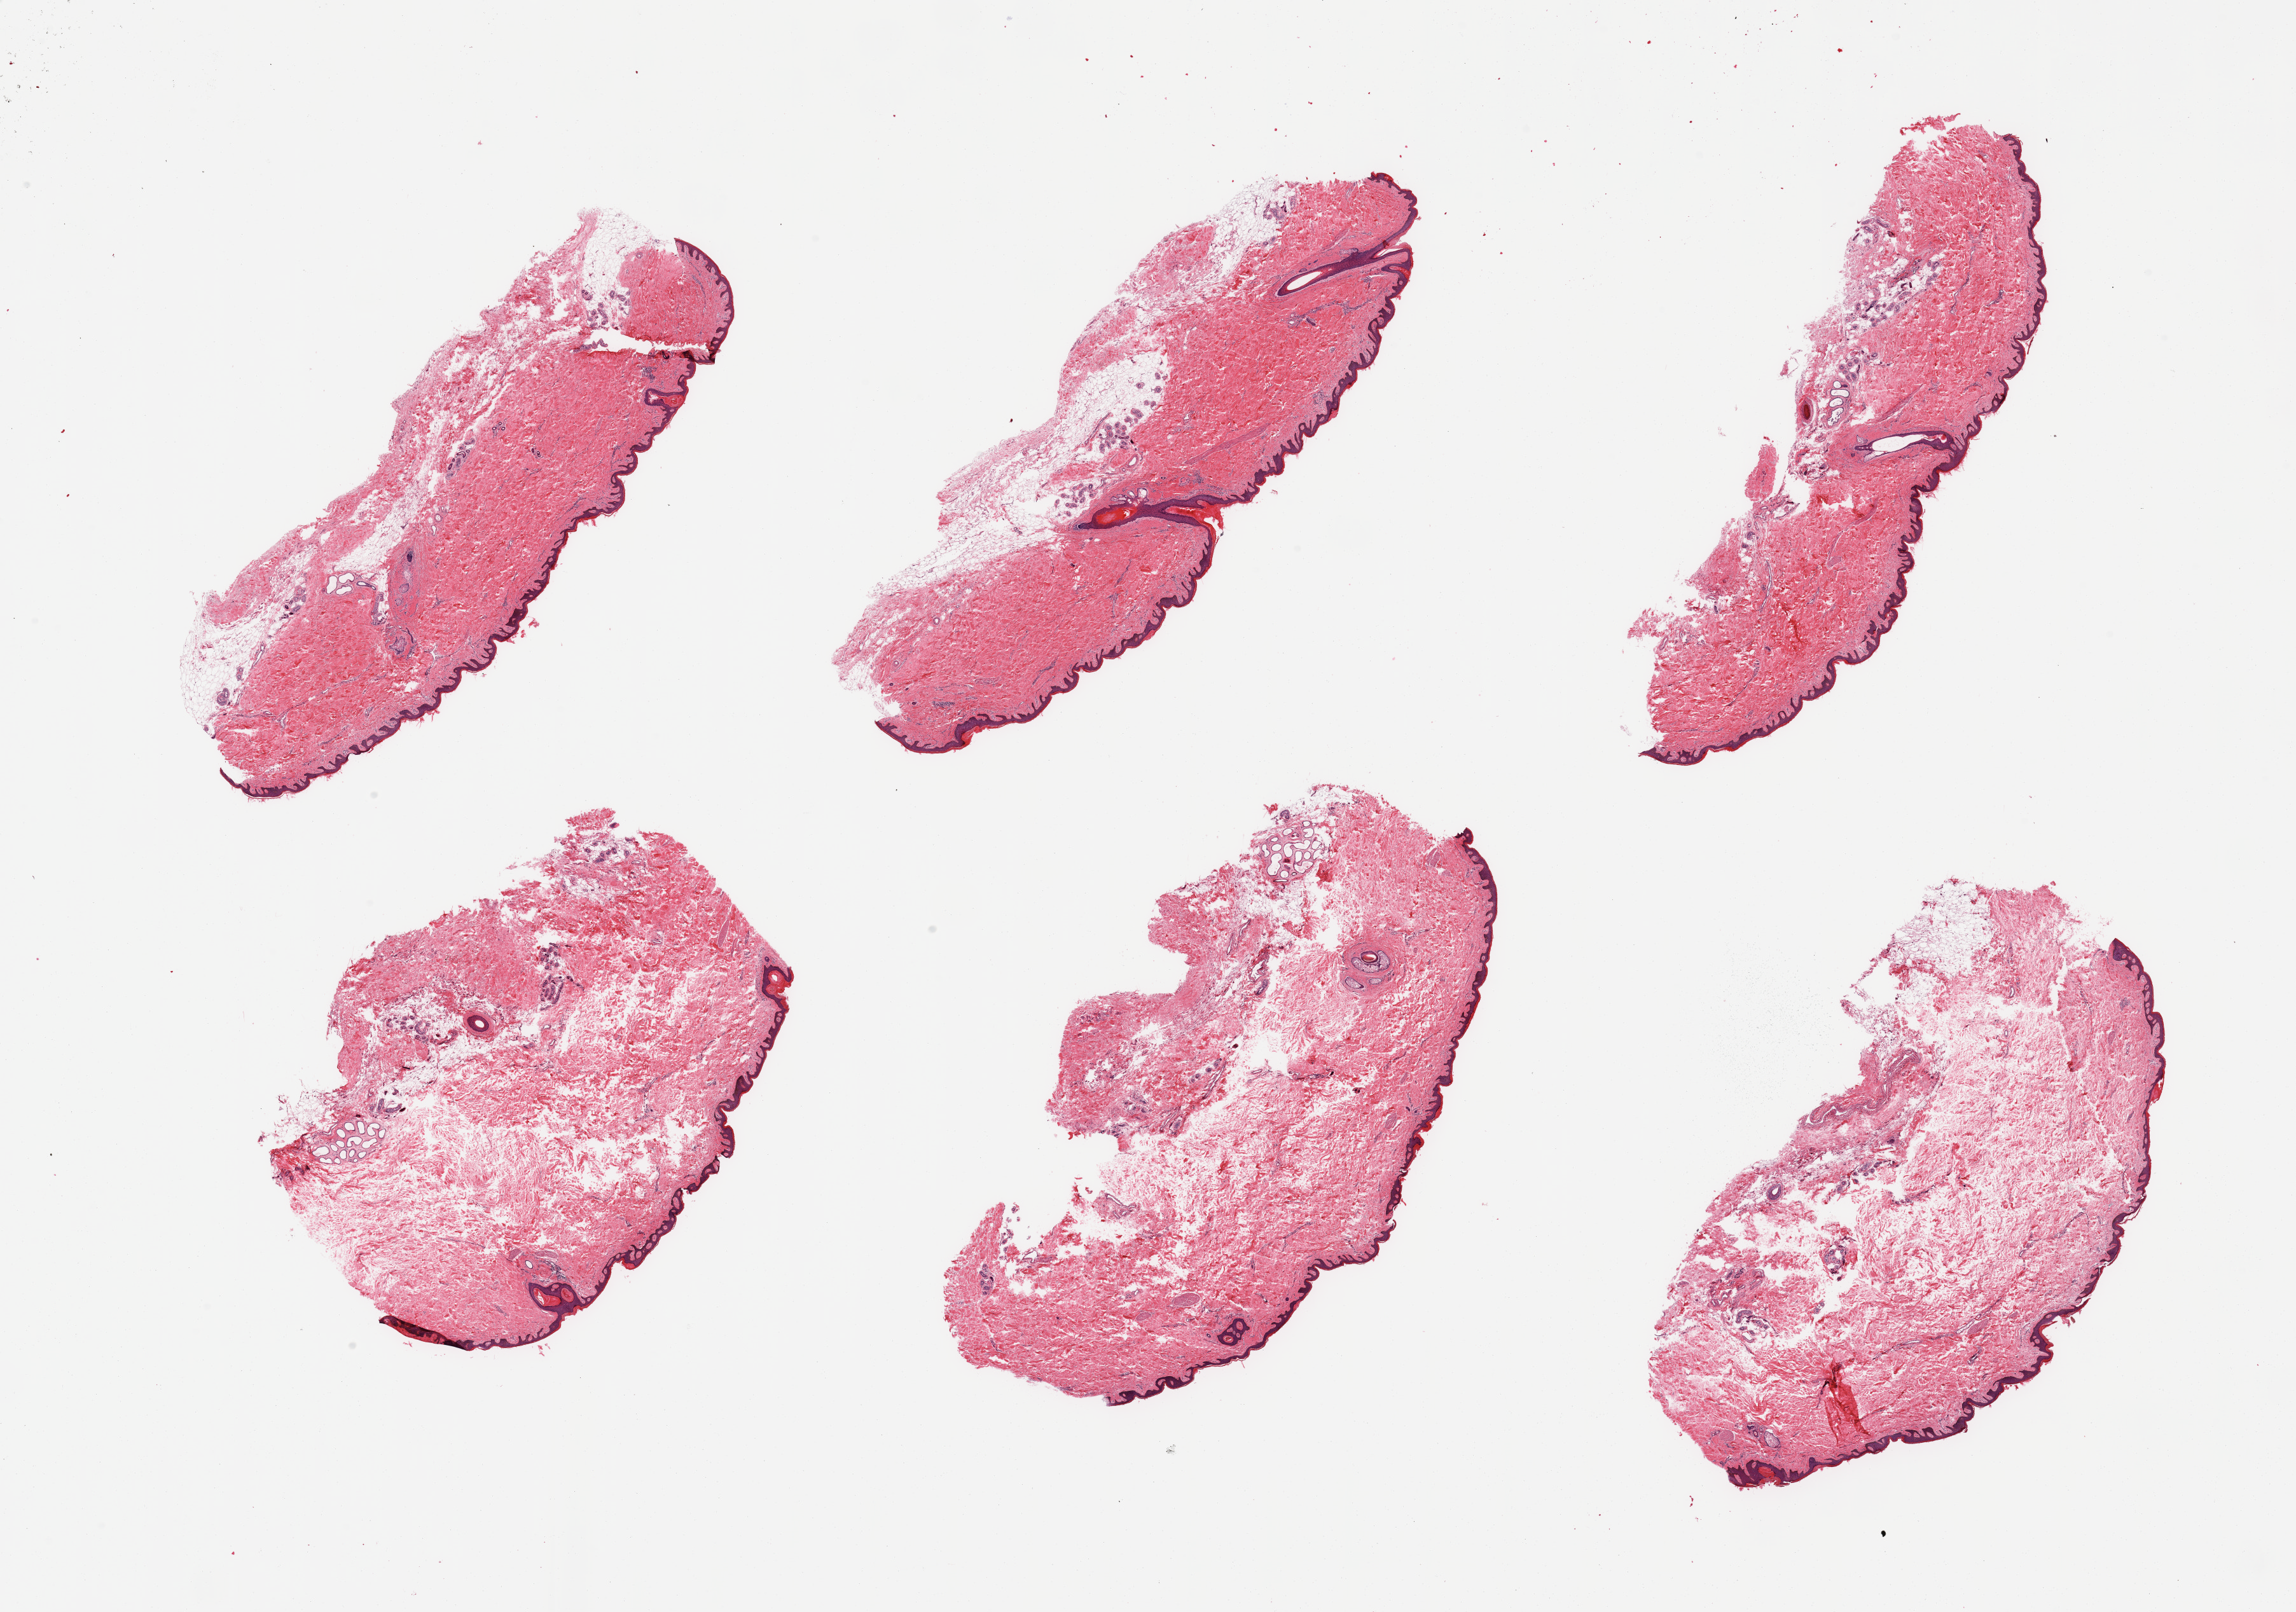
Whole-slide image, hematoxylin and eosin (H&E) stain — a low-resolution overview of the entire scanned area, about 28.5 x 20.0 mm (slide scanned at 20x), PAXgene-fixed paraffin-embedded (PFPE) section, section of skin of suprapubic region (target tissue), tissue donor sample. Donor sex: female.
Reviewer comment on this tissue sample: 6 pieces; 3 pieces well preserved, 3 have dermal edema.